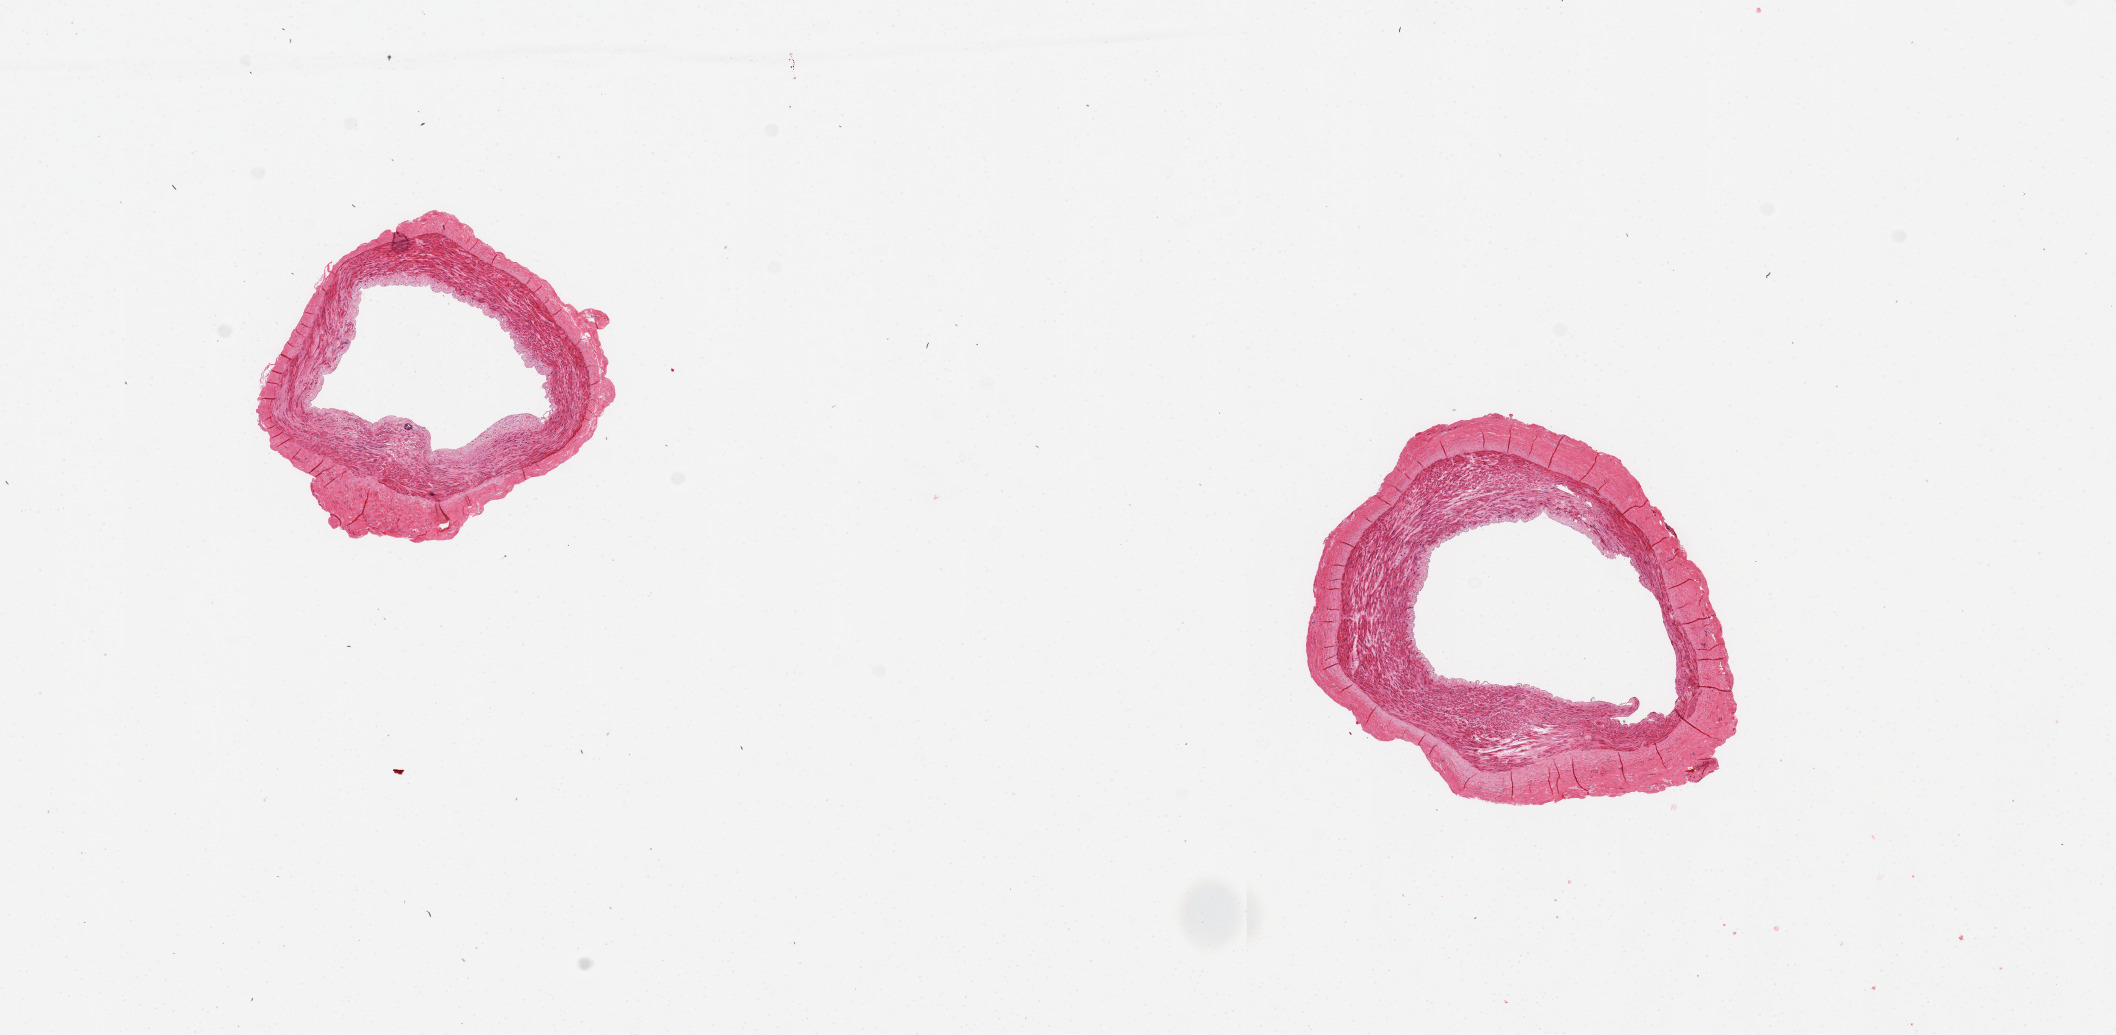
Haematoxylin and eosin whole-slide image, brightfield, whole scanned area (about 16.7 x 8.2 mm, from a 20x scan) shown as a low-resolution overview. PAXgene-fixed, paraffin-embedded tissue. Sampled site (target tissue): tibial artery. Tissue donor sample. Donor sex: female.
- pathologist's review note for this sample: 2 pieces, 3x2 & 3.5x3mm; so stroma, no lesions except for a minute calification